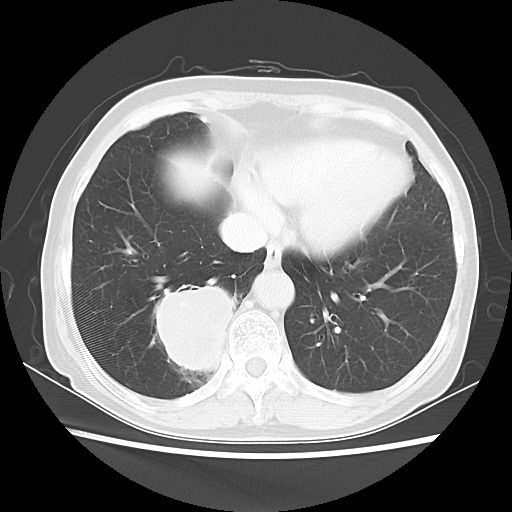
Chest CT, one axial slice. Position 16 of 56 along the scan axis. Reconstruction kernel LUNG. 120 kVp. Lung window (W 1500 / L -600 HU). 5 mm slice thickness. 512 × 512 image matrix, field of view 332 × 332 mm. Patient: female, 66 years. Case-level facts recorded for this patient, not image findings: clinical TNM (as recorded): T2 N3 M0.
Structures marked on this image (bounding box drawn by a radiologist):
- lung tumour (recorded histology: small cell carcinoma): bounding box <142,267,244,389> (left, top, right, bottom; pixels)